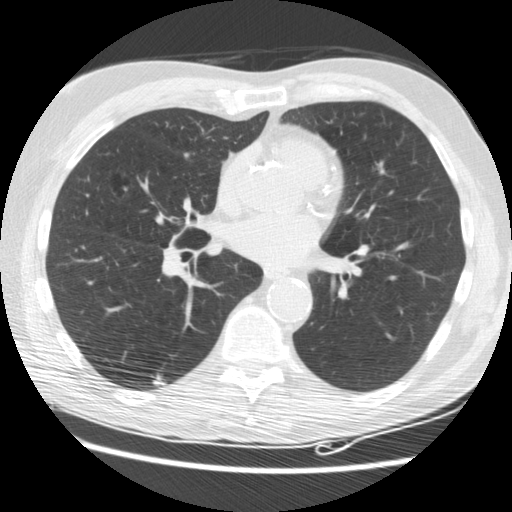
Chest CT (low-dose screening protocol), one axial image; third screening round (two years after baseline); lung window (W 1500 / L -600 HU). Male participant, aged 62 years at enrolment.
Lesion marked by an expert reader, bounding box [x1, y1, x2, y2] px = [144, 364, 176, 396]. The screening reader recorded 3 non-calcified nodules or masses ≥4 mm on this exam (right lower lobe, right lower lobe, right lower lobe); which of them this box marks is not recorded. Later outcome: lung cancer diagnosed 33 days after this screen — adenocarcinoma, NOS, right lower lobe, moderately differentiated (G2), stage IIIB (AJCC 6th edition), 15 mm at pathology.